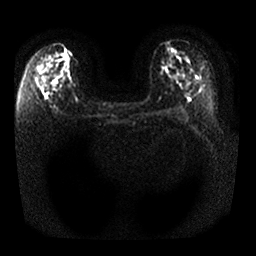
Breast MRI, one axial slice. Slice 14 of 25 in the series (ordered by position). Diffusion-weighted series; image 2 of 4 stored at this slice position (different b-values; order by instance number). 1.5 T. 4 mm slice thickness. 256 × 256 image matrix. Female patient.
Annotated regions visible in this slice (manually delineated by an expert):
- tumour on diffusion-weighted imaging: box from (x=39, y=74) to (x=53, y=88) px